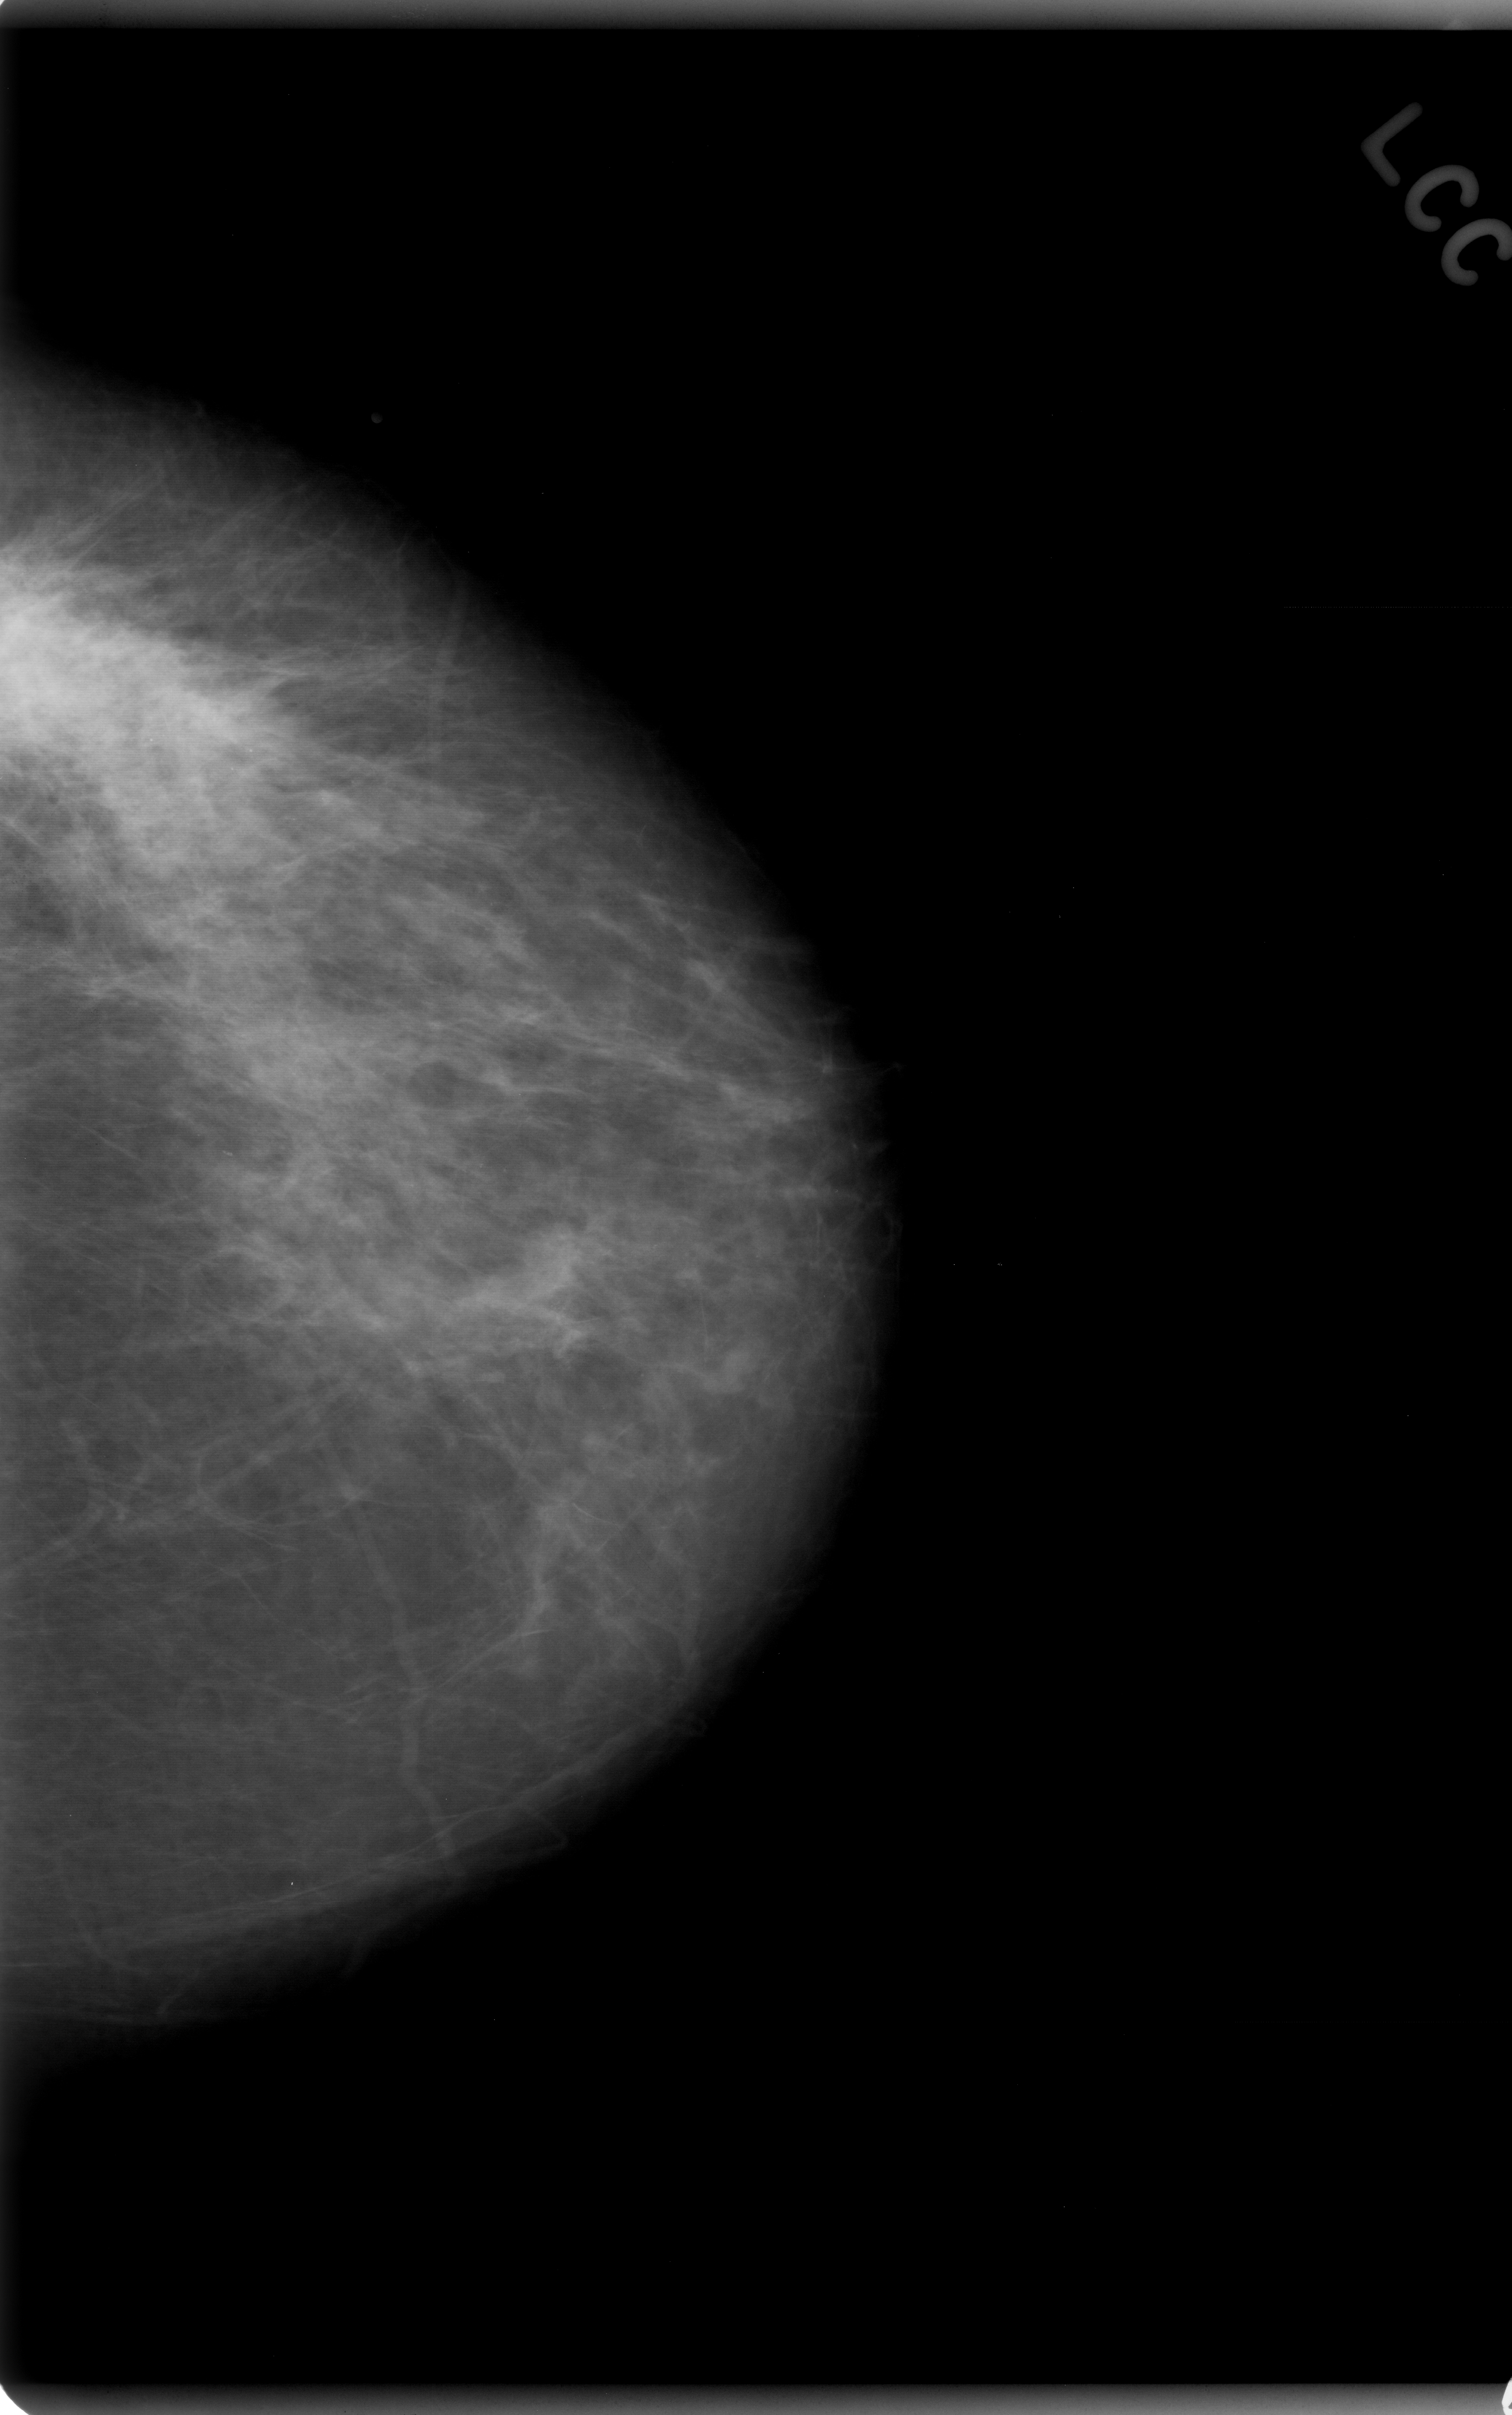
Digitized screen-film mammogram, left breast, craniocaudal (CC) view, BI-RADS breast density category 2 (scale 1–4).
- Marked findings (only marked abnormalities are described; nothing is implied about the rest of the image): calcifications, morphology pleomorphic, distribution regional; BI-RADS assessment category 4; subtlety rating 2 on a 1 (subtle) to 5 (obvious) scale; pathology result (as recorded, not read from the image): malignant.